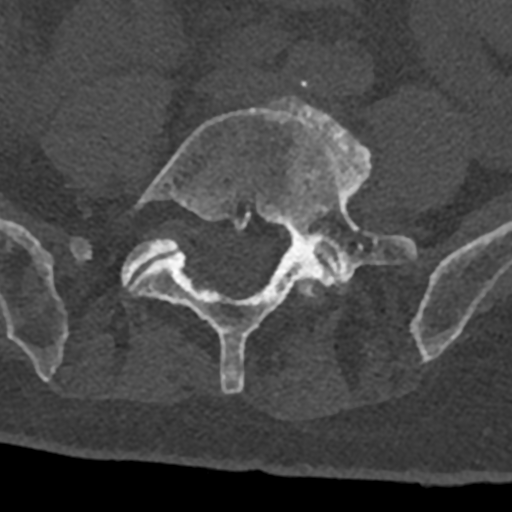
CT including the spine, one axial slice. Slice 201 of 797 in the series (ordered by position). Reconstruction kernel Br40s/3. 120 kVp. Bone window (W 1800 / L 400 HU). 0.5 mm slice thickness. 512 × 512 image matrix, field of view 160 × 160 mm. Male patient, age 74 years. From the clinical record (not read from this slice): primary cancer: renal.
Annotated regions visible in this slice (semi-automatic segmentation, software-assisted and operator-edited):
- L4 vertebra: bounding box (x1, y1, x2, y2) in pixels: (291, 278, 317, 298)
- L5 vertebra: (130, 96, 417, 394)